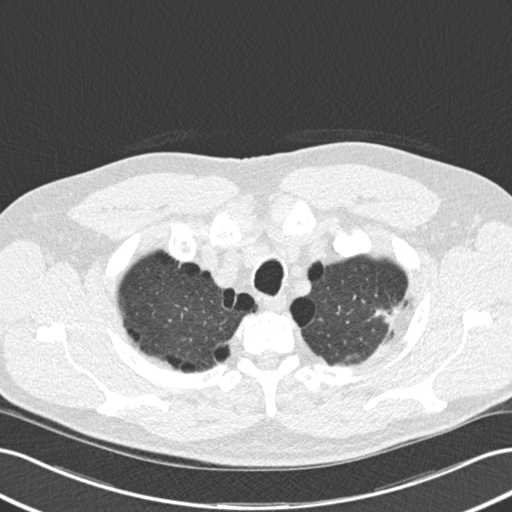
Low-dose screening chest CT, one axial slice; position 145 of 177 along the scan axis; 120 kVp; lung window (W 1500 / L -600 HU); 512 × 512 image matrix, field of view 360 × 360 mm.
Outlined on this slice (outlined manually by an expert reader):
- lesion 1 (tumor, upper lobe of left lung): bounding box (x1, y1, x2, y2) in pixels: (375, 306, 398, 323)